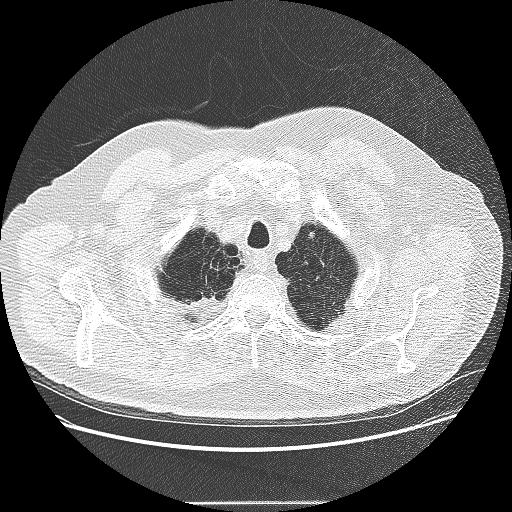
Low-dose screening chest CT, one axial slice; slice 224 of 265 in the series (ordered by position); lung window (W 1500 / L -600 HU); 512 × 512 image matrix, field of view 400 × 400 mm.
Structures marked on this image (expert manual segmentation):
- lesion 1 (tumor, upper lobe of left lung): bounding box <308,232,314,238> (left, top, right, bottom; pixels)